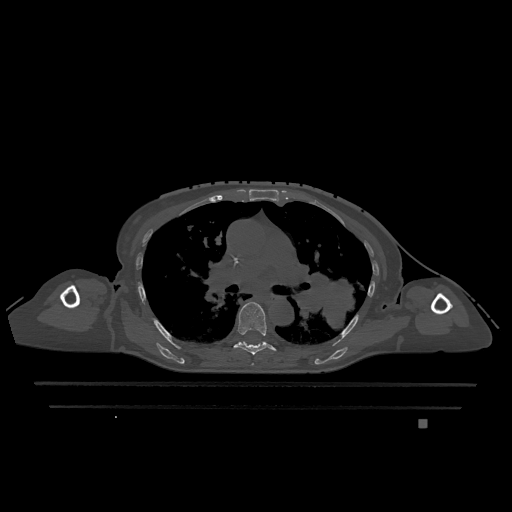
CT including the spine, one axial slice; position 787 of 1317 along the scan axis; bone window (W 1800 / L 400 HU); 0.5 mm slice thickness; 512 × 512 image matrix, field of view 500 × 500 mm. Female patient, age 74 years. From the clinical record (not read from this slice): primary cancer: lung.
Structures marked on this image (semi-automatic segmentation, software-assisted and operator-edited):
- T5 vertebra: bounding box [x1, y1, x2, y2] px = [252, 363, 254, 366]
- T6 vertebra: [234, 302, 276, 355]